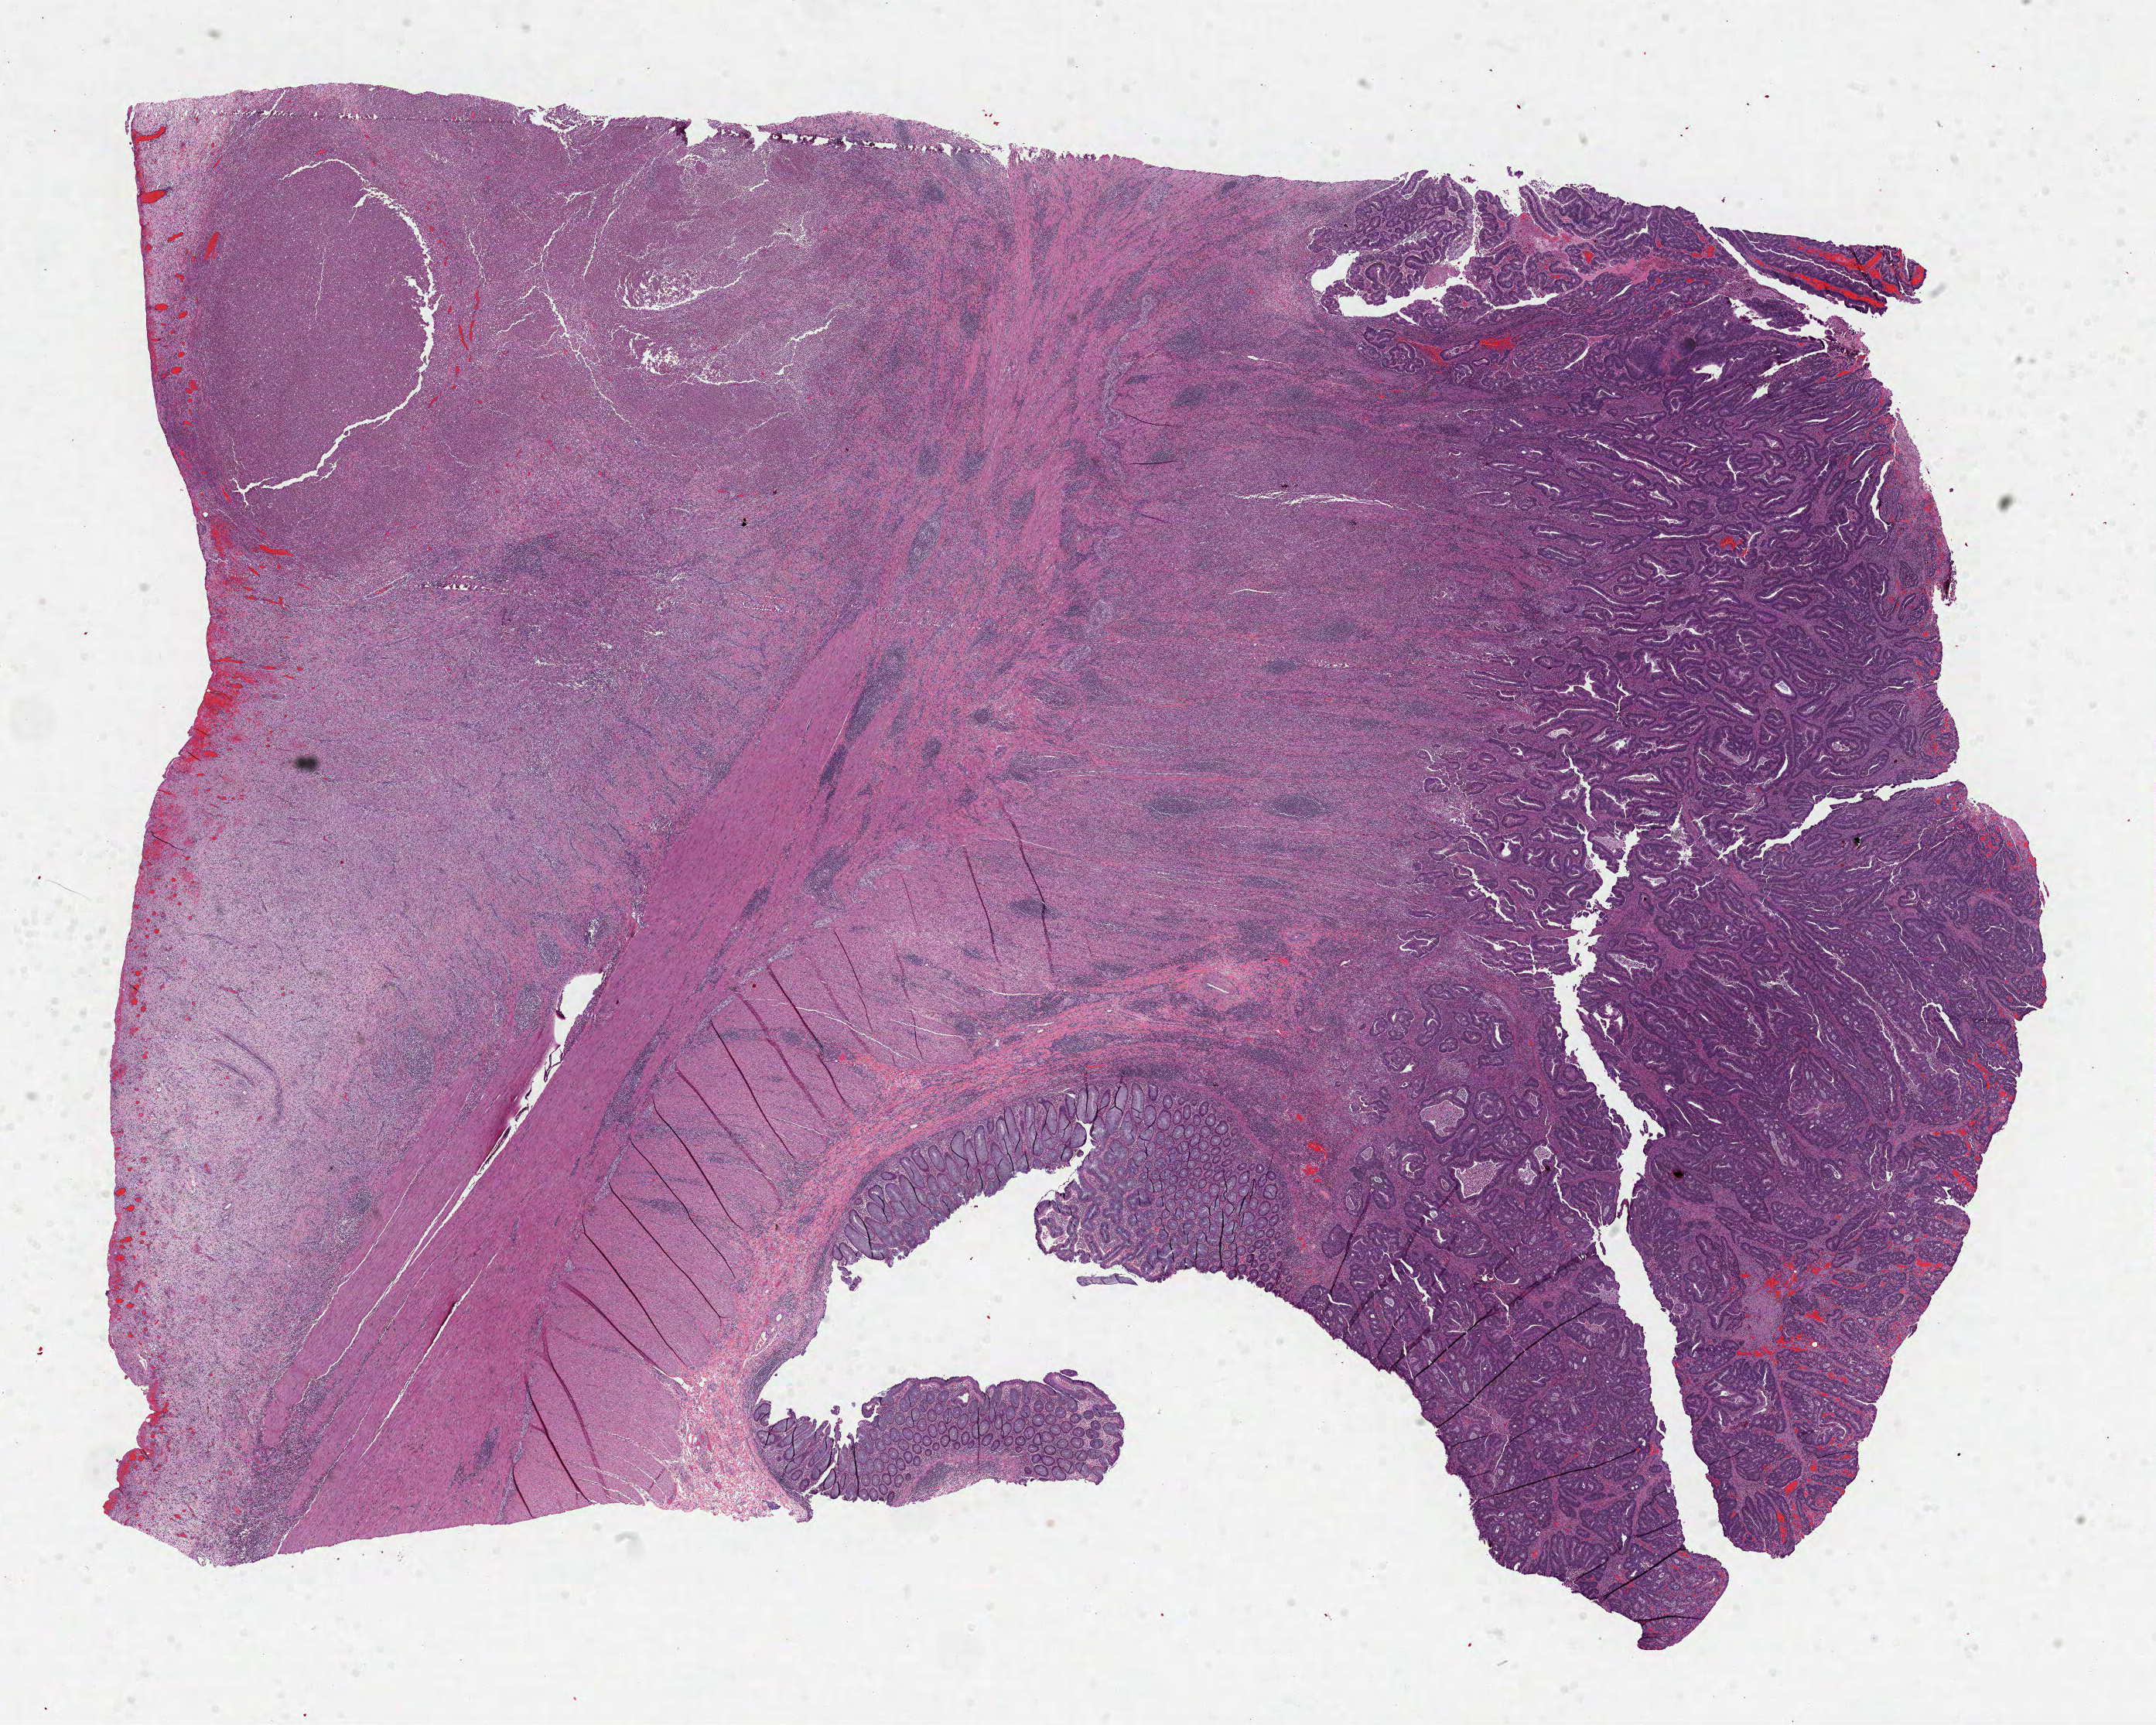
H&E whole-slide image, low-resolution overview of the scanned area, about 22.5 x 18.0 mm (acquisition: 40x scan). Formalin-fixed paraffin-embedded (FFPE) diagnostic section. Rectum, primary tumour sample. Male patient; age at initial diagnosis 43 years.
Diagnosis: Adenocarcinoma, NOS (rectosigmoid junction).